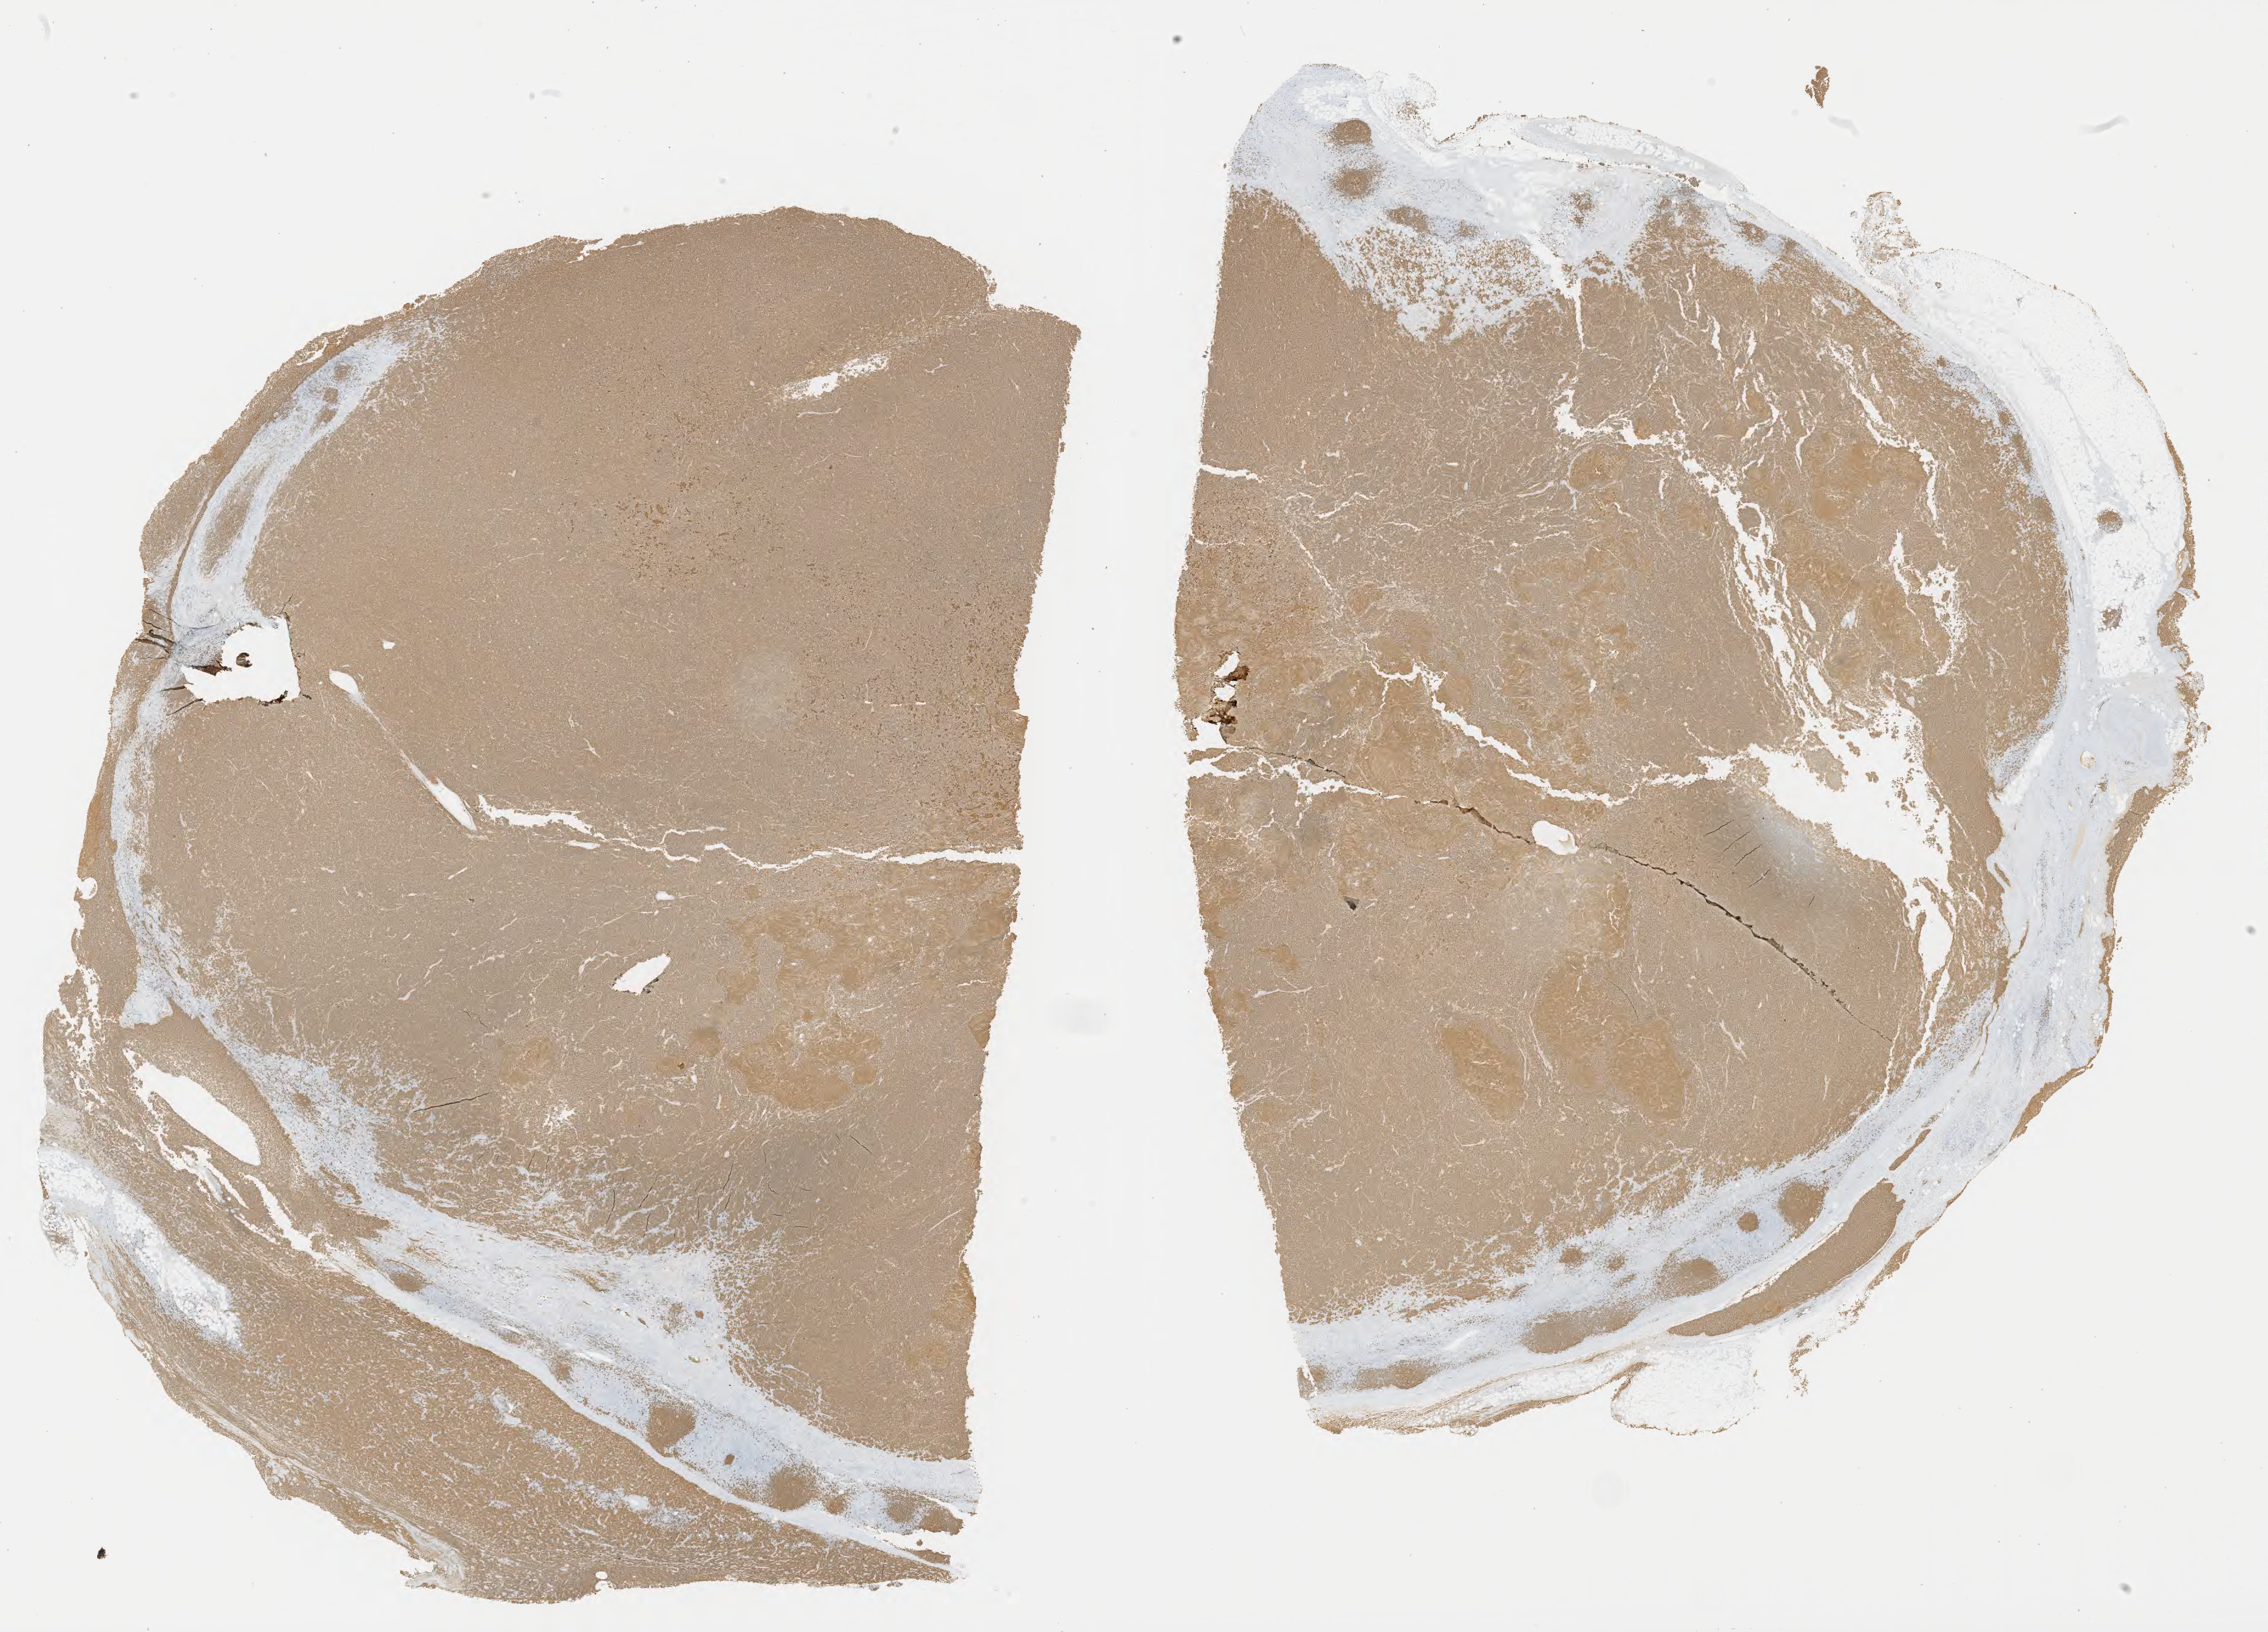
Whole-slide image, immunohistochemical stain for CD20, a low-resolution overview of the entire scanned area, about 30.2 x 21.7 mm, specimen: tumor tissue. Patient male; aged 48.
Histologic diagnosis: Burkitt lymphoma, NOS.